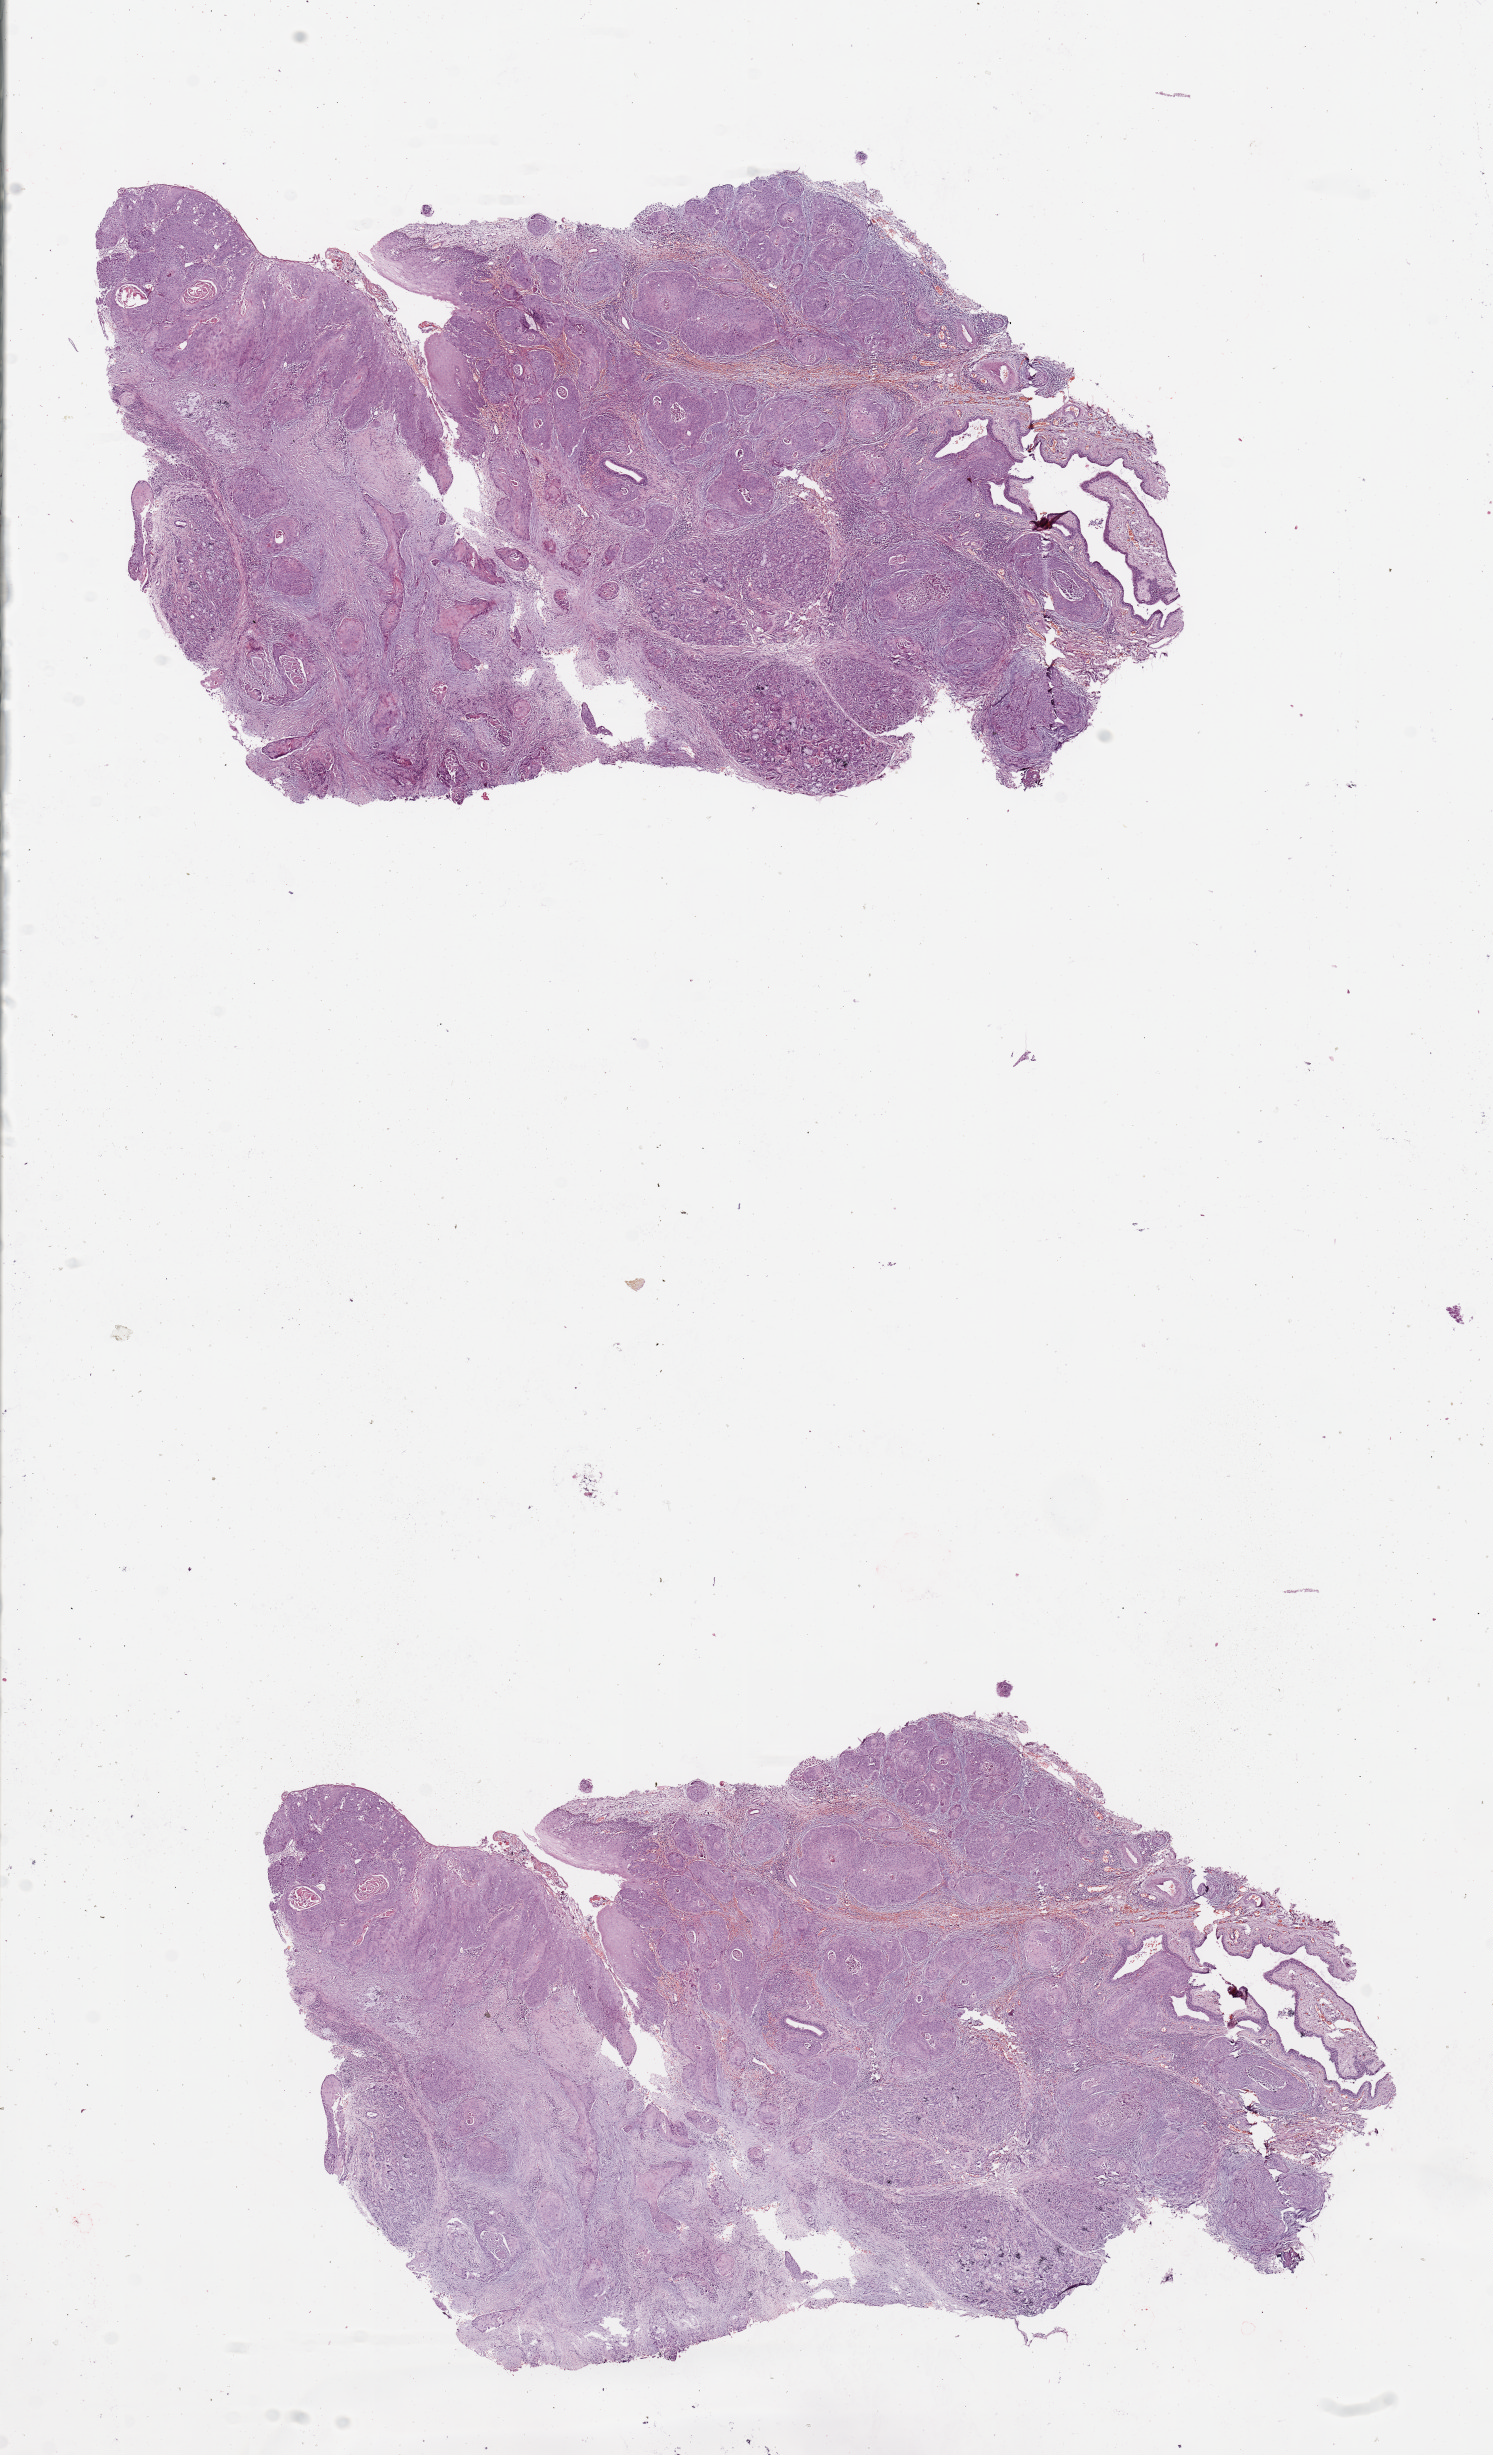
Digitized H&E tissue section (whole slide), a low-resolution overview of the entire scanned area, about 11.8 x 19.4 mm, head and neck, tissue type not recorded. Patient: male, age 58 years.
- patient diagnosis: Squamous cell carcinoma, NOS (floor of mouth, NOS)